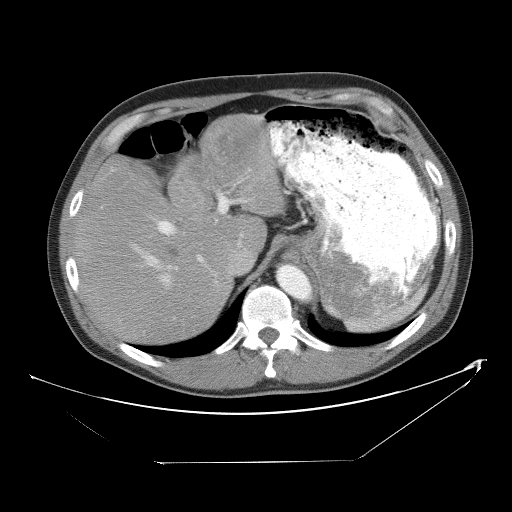
Contrast-enhanced abdominal CT, one axial slice. Position 38 of 53 along the scan axis. 120 kVp. Intravenous contrast given. Soft-tissue window (W 400 / L 40 HU). 5 mm slice thickness. 512 × 512 image matrix, field of view 438 × 438 mm. Male patient, age 59 years. From the clinical record (not read from this slice): diagnosis: colorectal cancer liver metastases, imaged before liver resection.
Structures marked on this image (outlined manually by an expert reader):
- hepatic veins: box from (x=132, y=244) to (x=178, y=288) px
- liver: (x=77, y=118)–(x=283, y=343)
- planned liver remnant (the part of the liver to remain after resection): (x=76, y=161)–(x=234, y=343)
- portal vein (with intrahepatic branches): (x=150, y=193)–(x=249, y=262)
- liver metastasis: (x=167, y=246)–(x=181, y=261)
- liver metastasis: (x=192, y=133)–(x=257, y=179)